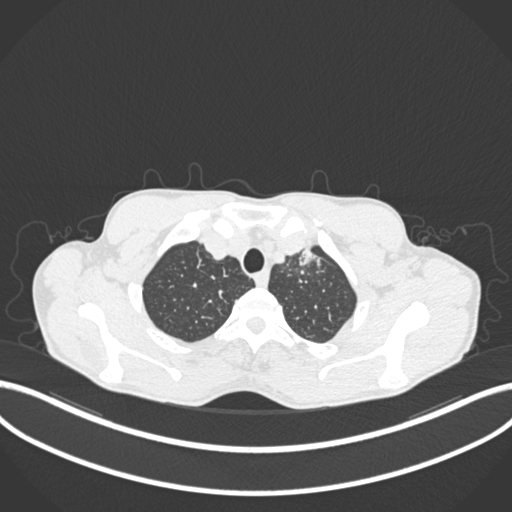
Chest CT, one axial slice; slice 181 of 211 in the series (ordered by position); reconstruction kernel B30f; lung window (W 1500 / L -600 HU); 1 mm slice thickness; 512 × 512 image matrix, field of view 400 × 400 mm. Patient: male, 58 years. From the clinical record (not read from this slice): clinical TNM (as recorded): T1c N1 M0.
Annotated regions visible in this slice (bounding box drawn by a radiologist):
- lung tumour (recorded histology: adenocarcinoma): box from (x=295, y=241) to (x=322, y=269) px